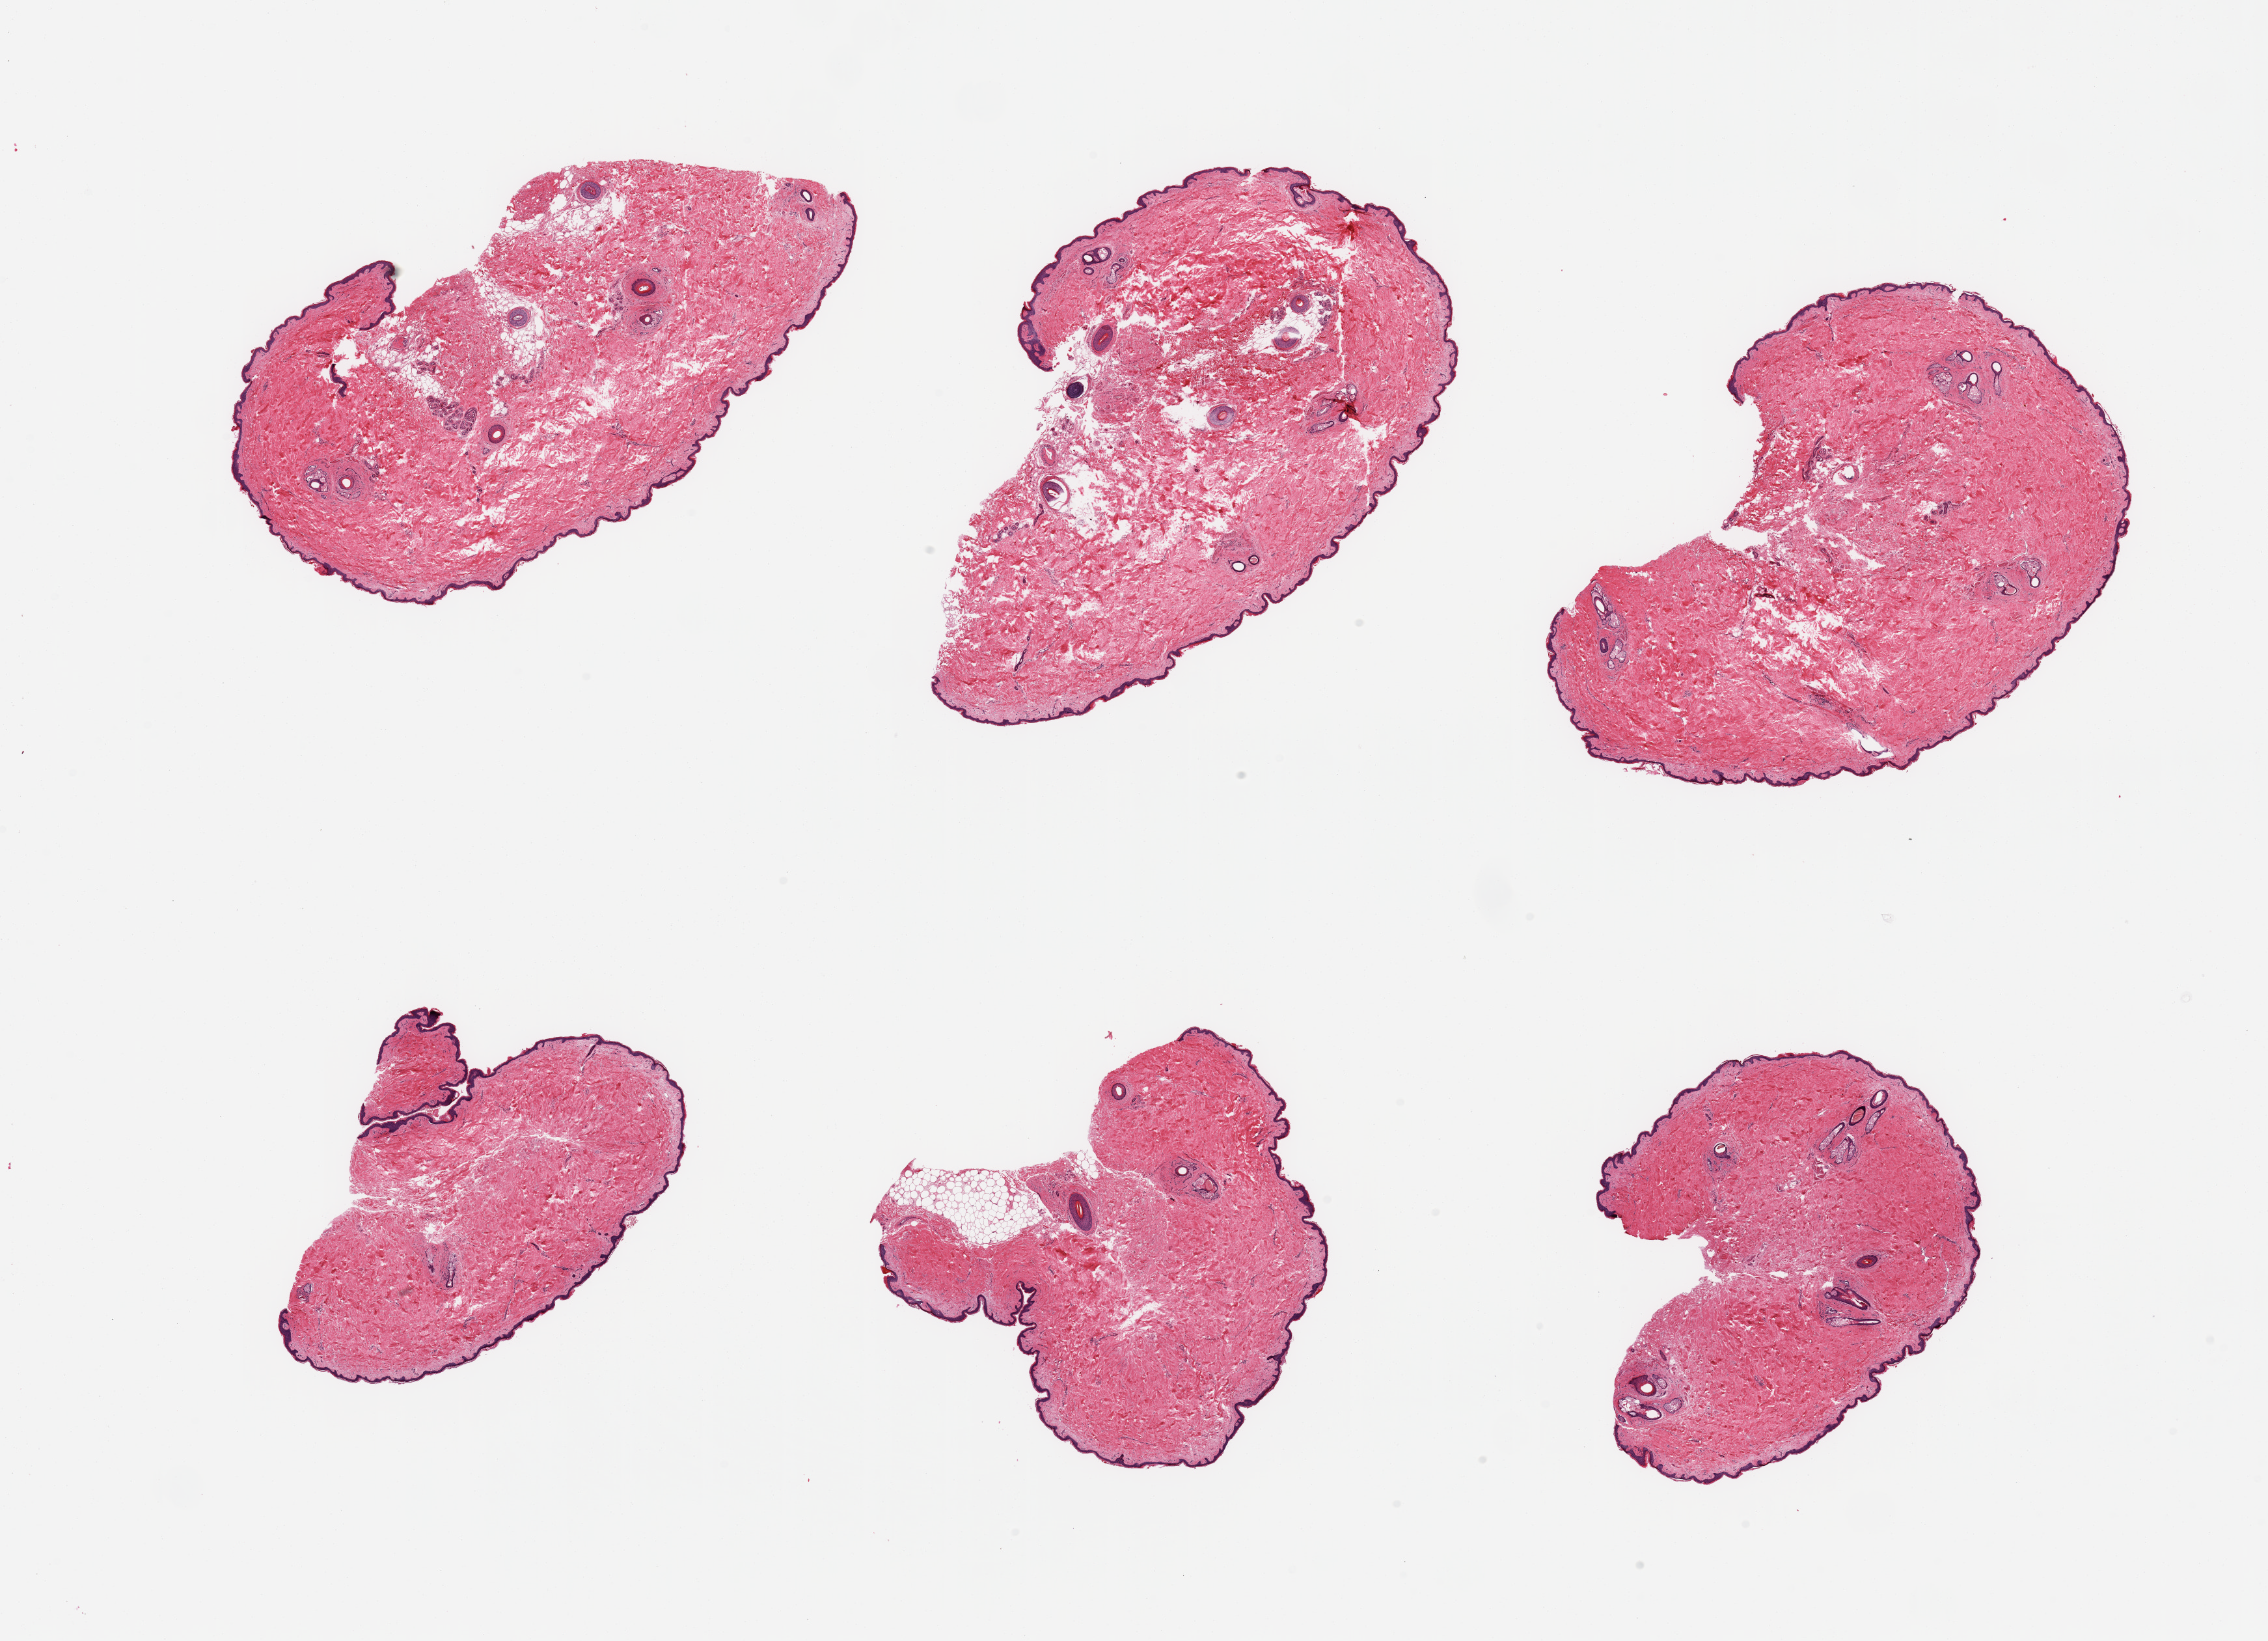
Hematoxylin and eosin (H&E) whole-slide image — whole scanned area (about 27.6 x 19.9 mm, slide scanned at 20x) shown as a low-resolution overview. Donor: male.
• specimen: PAXgene-fixed, paraffin-embedded tissue; target tissue: skin of suprapubic region; donor tissue sample